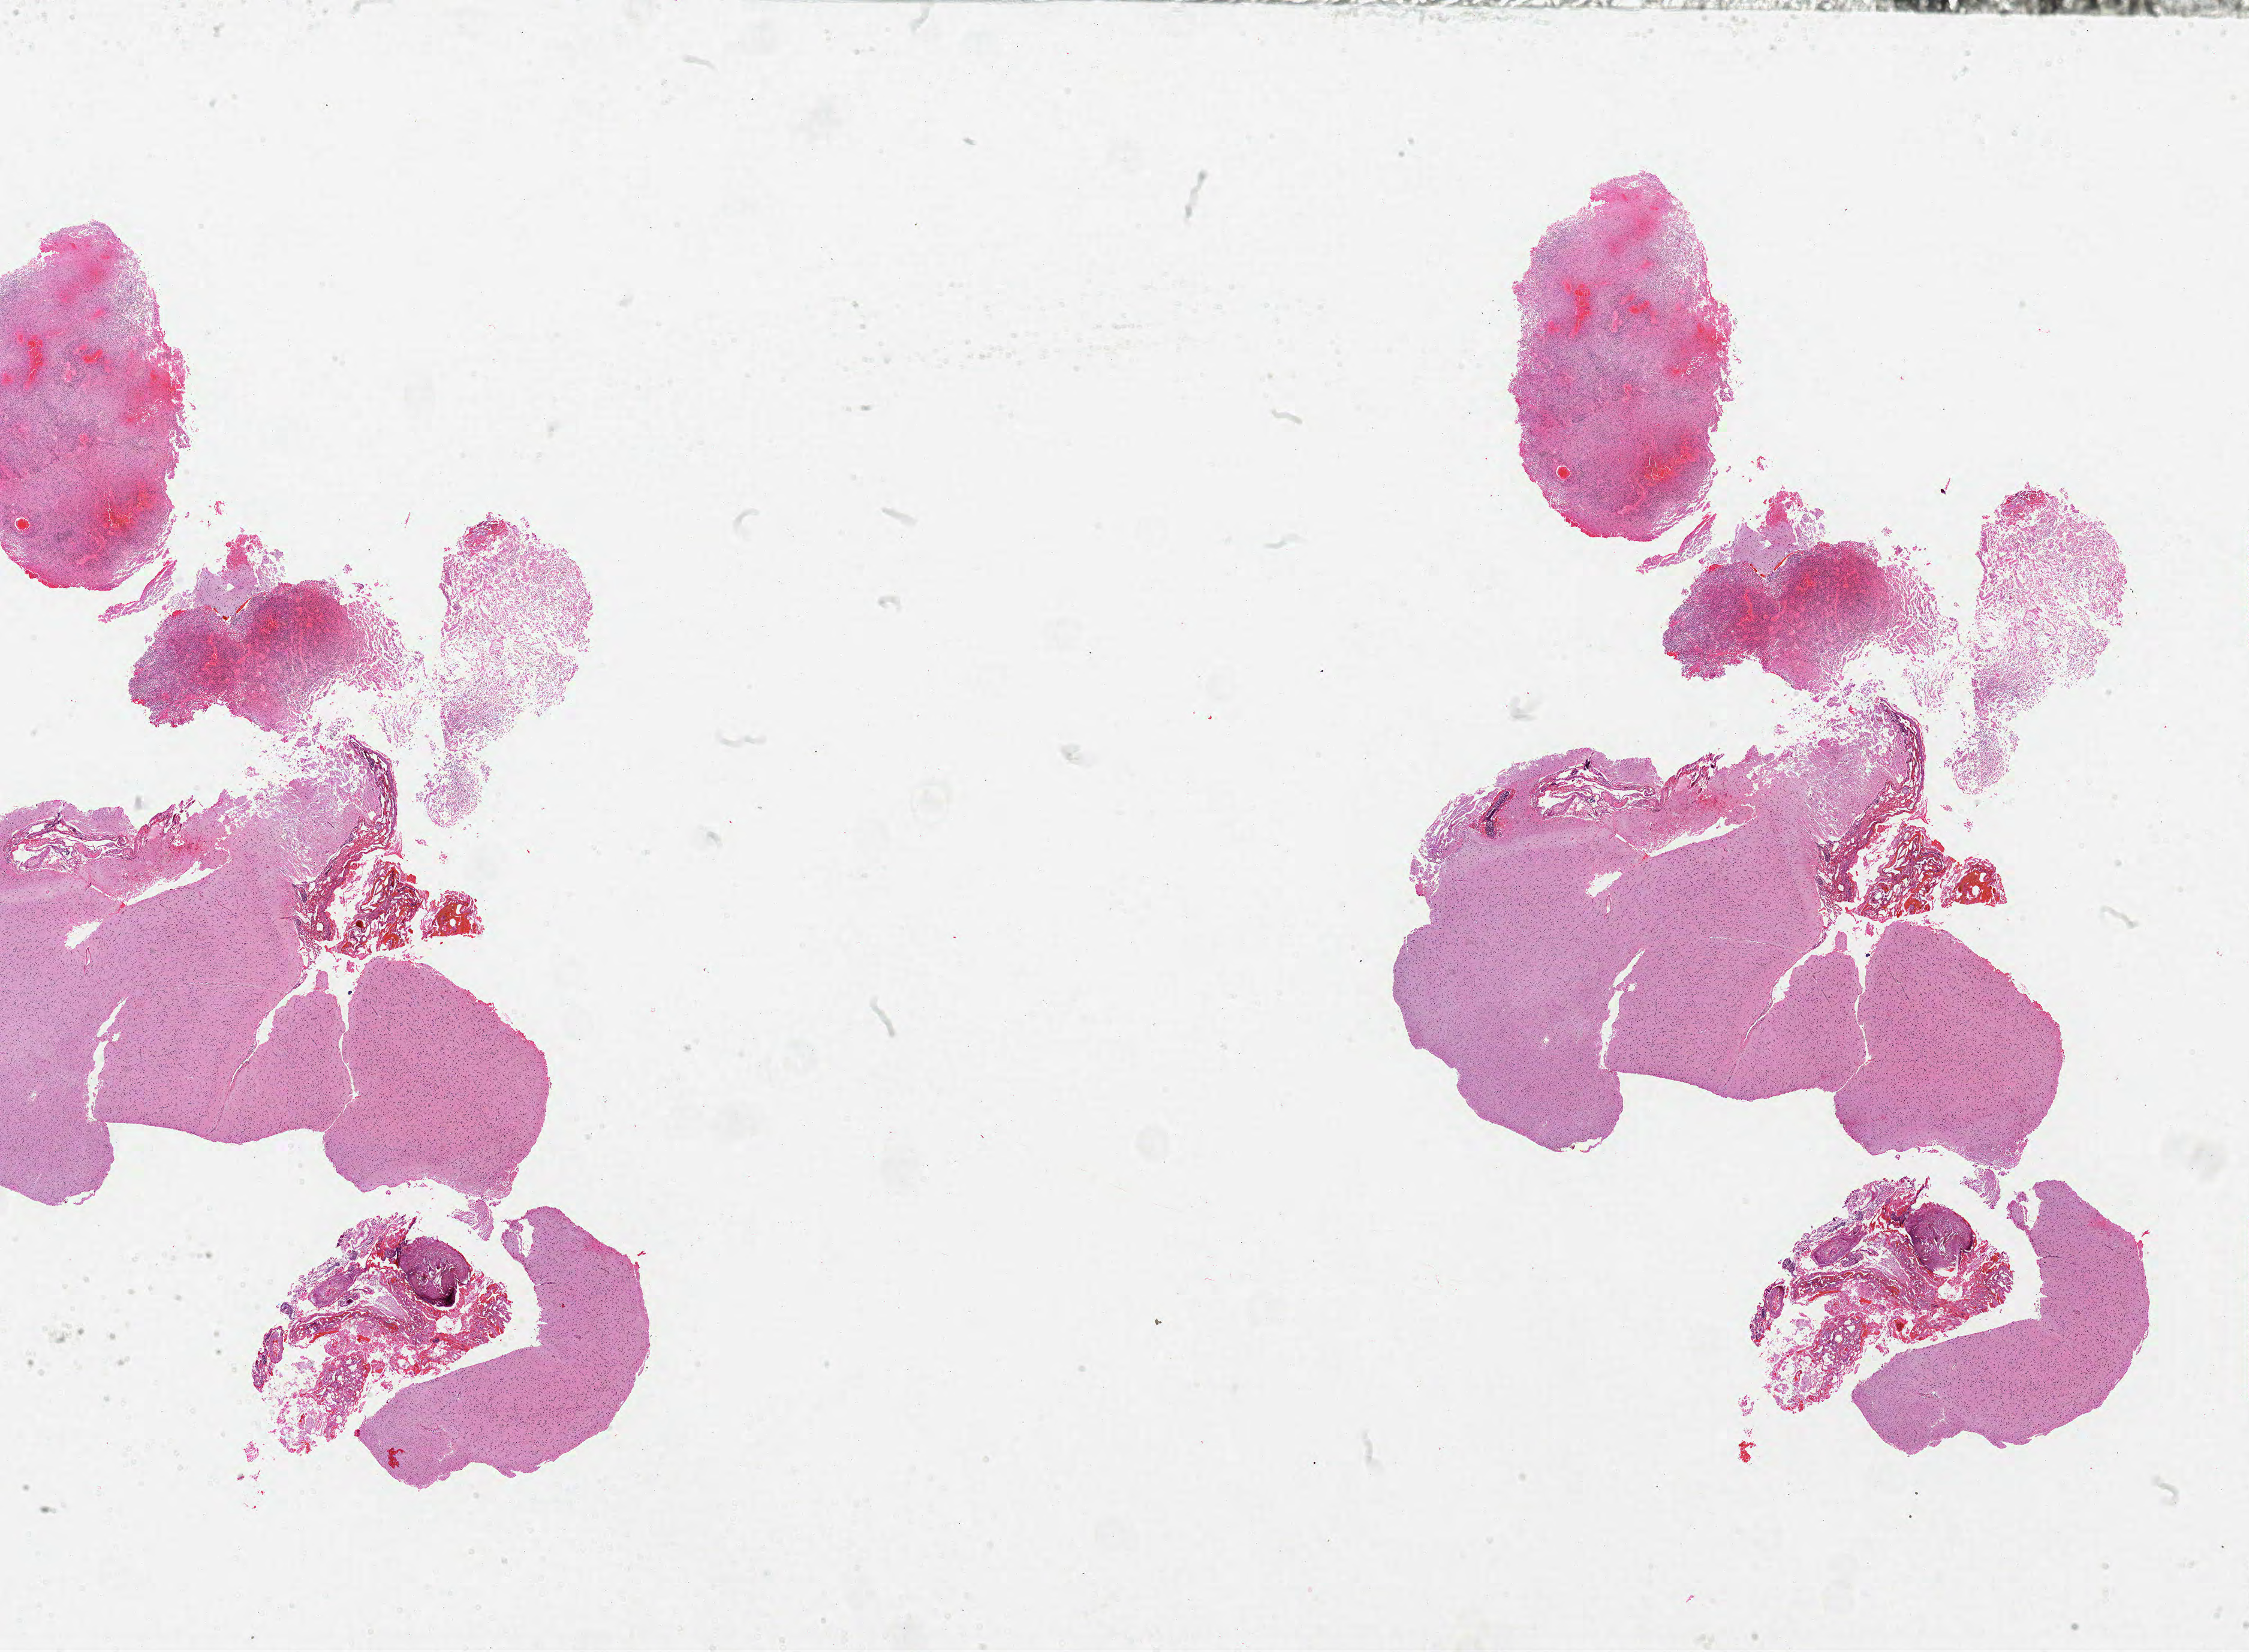
H&E whole-slide image, a low-resolution overview of the entire scanned area, about 30.0 x 22.0 mm, formalin-fixed paraffin-embedded (FFPE) diagnostic section, brain, primary tumour sample. Male, age 69 years at initial diagnosis.
* diagnosis: Glioblastoma